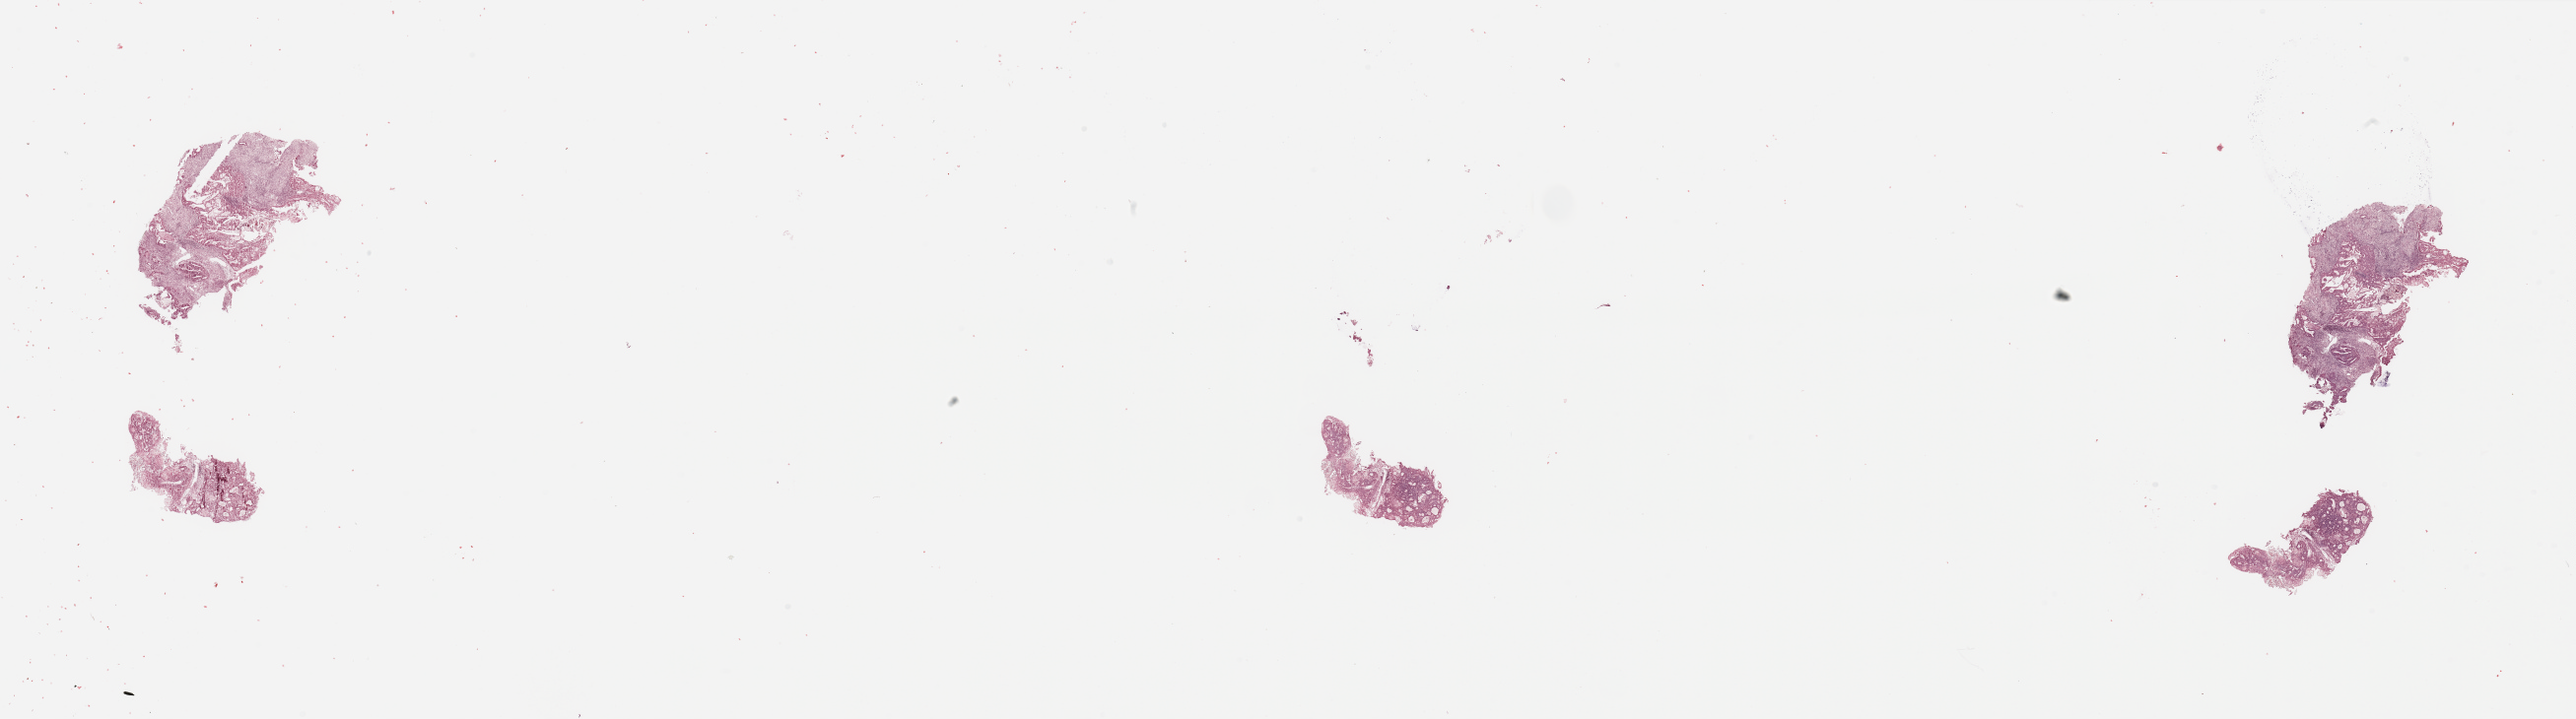
Whole-slide histology image, Hematoxylin and eosin (H&E) stained — a low-resolution overview of the entire scanned area, about 41.3 x 11.5 mm. Tumour tissue sample, uterus. 80-year-old female patient. Histologic grade: G2 (moderately differentiated).
Histologic diagnosis: Endometrioid adenocarcinoma, NOS. AJCC pathologic stage: I. Primary tumour site (as recorded): anterior endometrium.